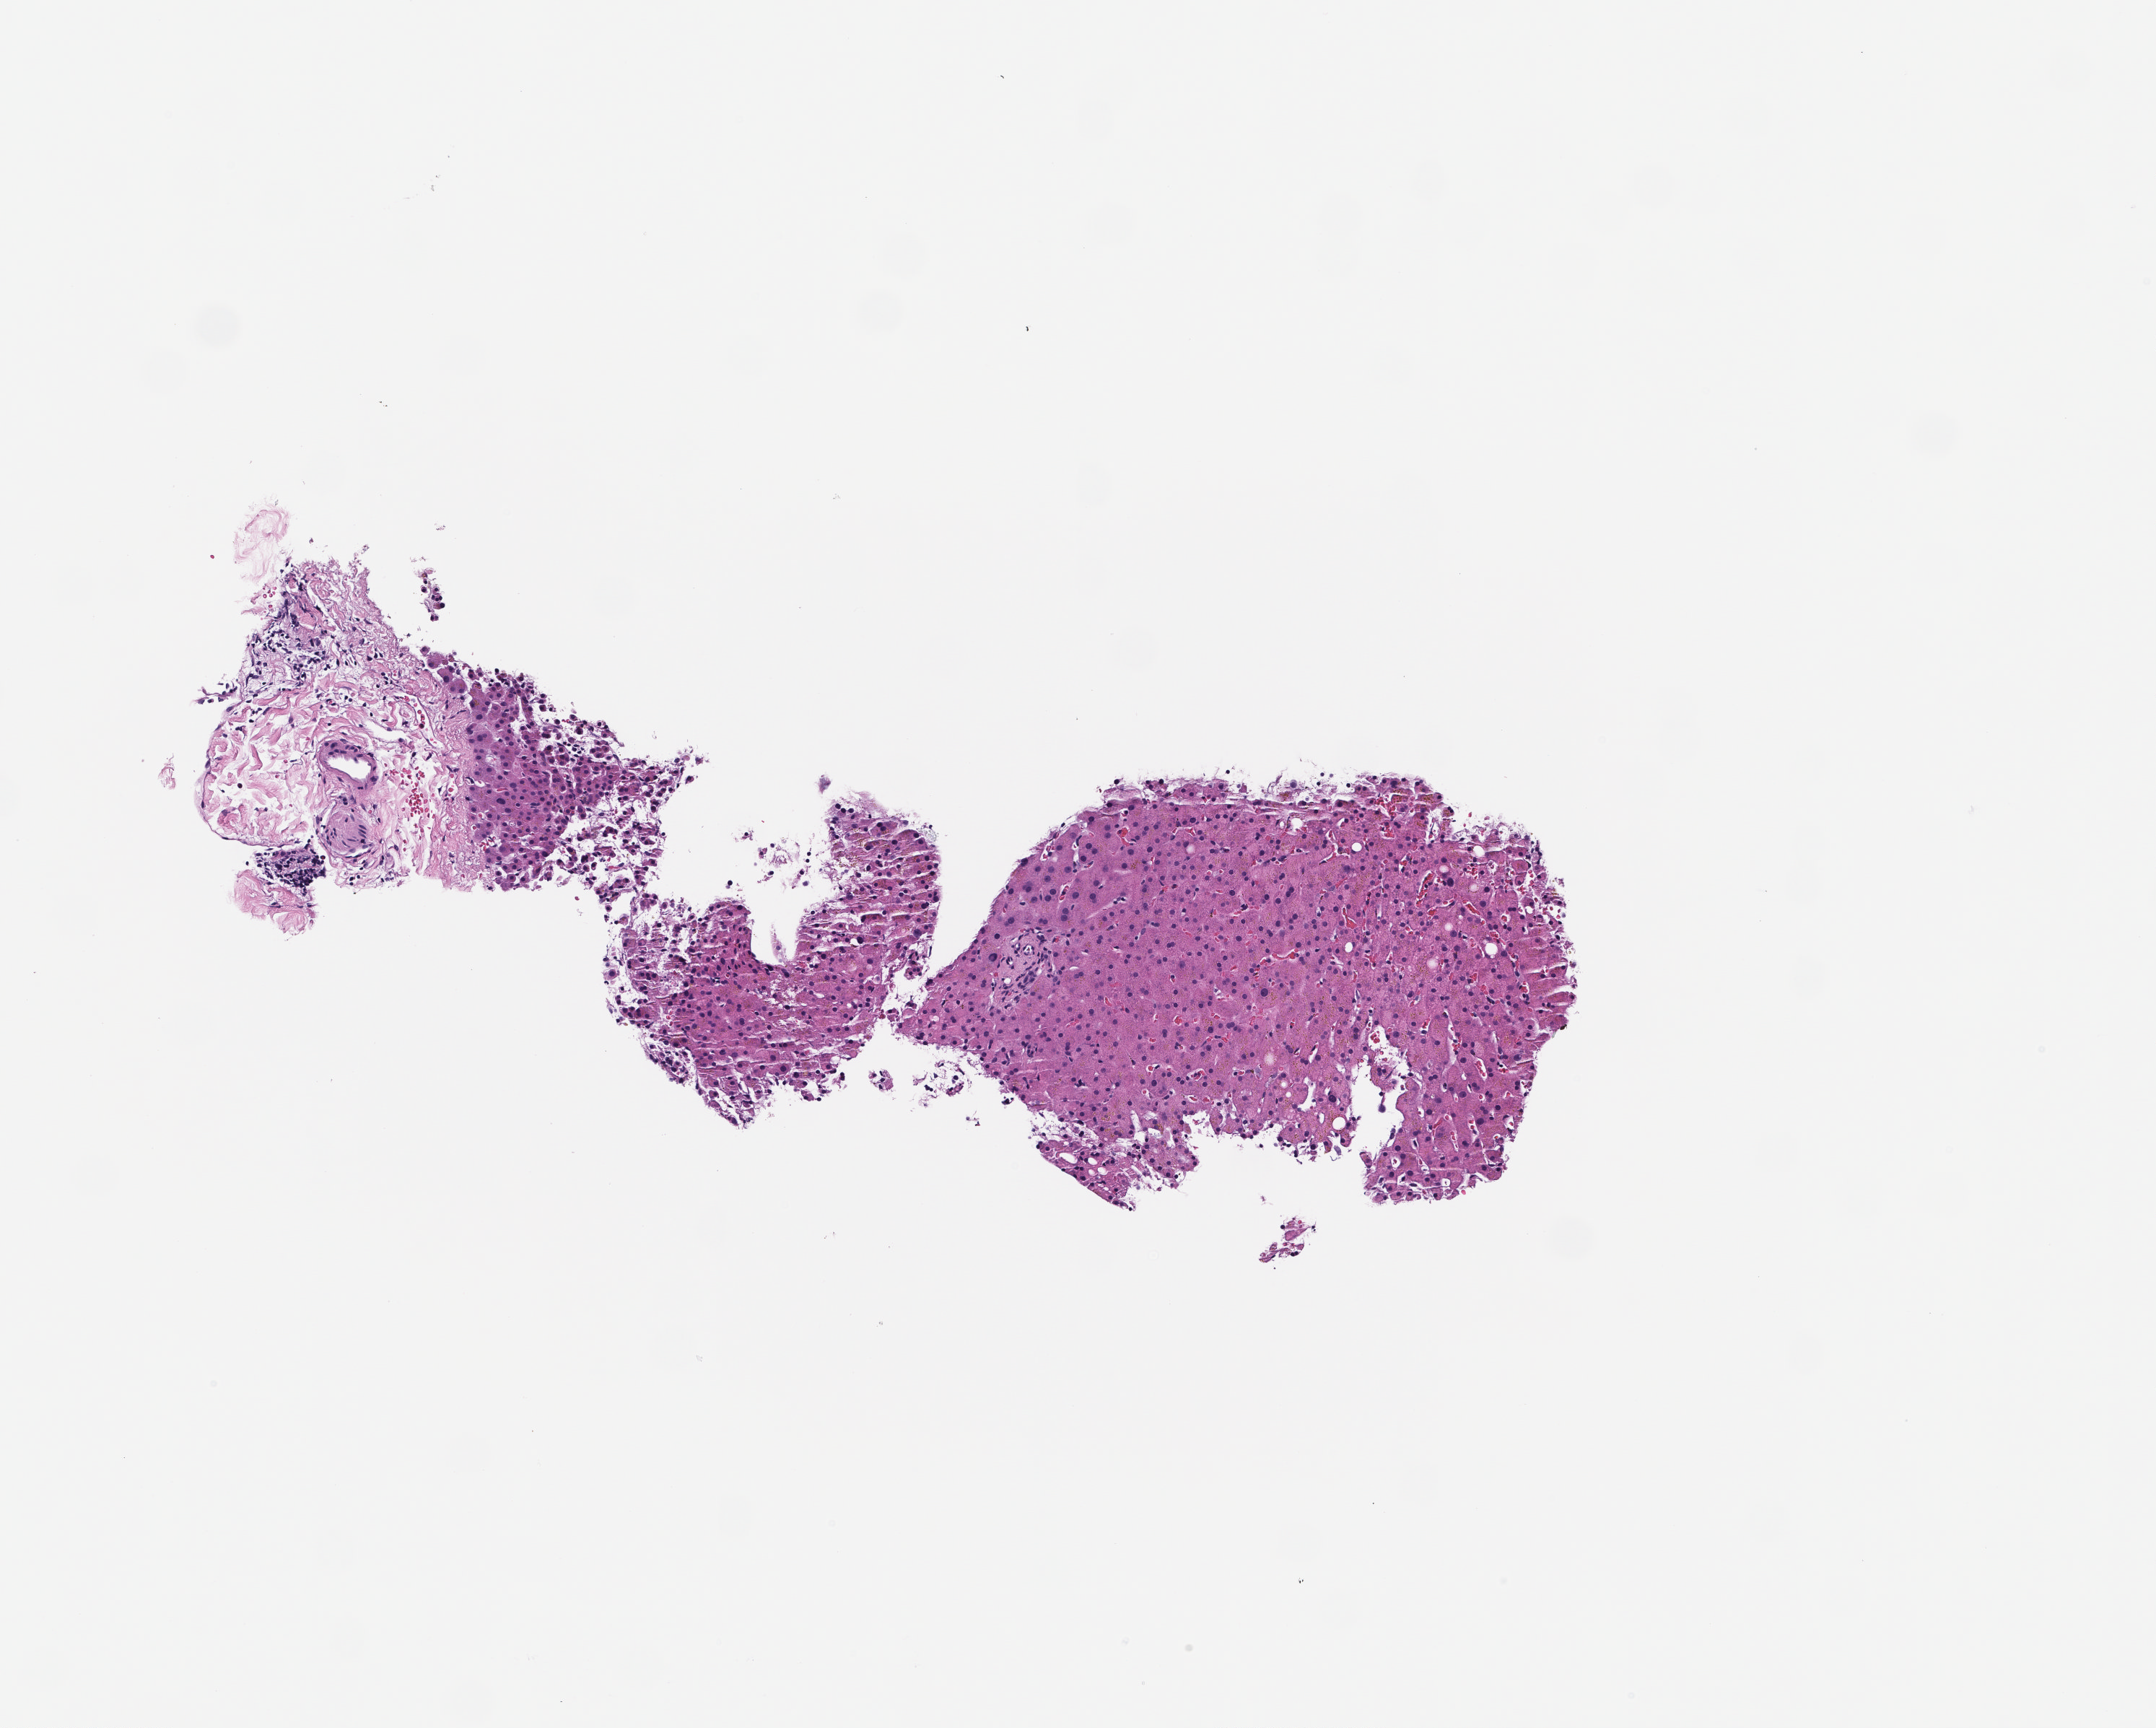
Hematoxylin and eosin (H&E) whole-slide image, low-resolution overview of the scanned area, about 3.0 x 2.4 mm. Formalin-fixed paraffin-embedded section. Specimen time point: collected at disease progression. Patient: female.
* this section: metastatic tumor tissue
* primary diagnosis of the patient: Non-Small Cell Lung Carcinoma